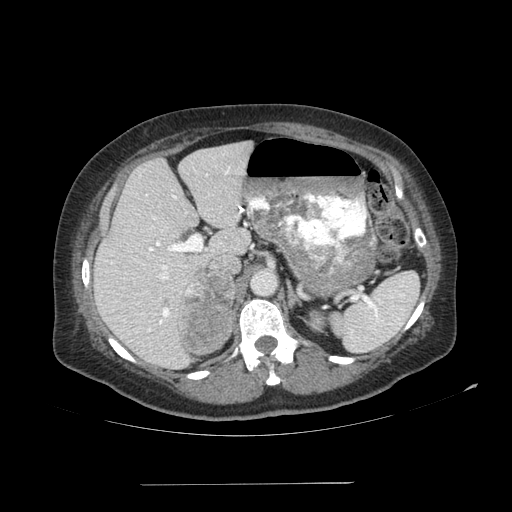
Contrast-enhanced abdominal CT, one axial slice. Position 68 of 113 along the scan axis. Reconstruction kernel SOFT. Soft-tissue window (W 400 / L 40 HU). 2.5 mm slice thickness. 512 × 512 image matrix. Patient: female, 67 years. Case-level facts recorded for this patient, not image findings: diagnosis: adrenocortical carcinoma; tumour side: right adrenal; tumour size at pathology: 9.8 cm; Ki-67 index: 59 %; stage (as recorded): 4.
Annotated regions visible in this slice (semi-automatic segmentation, software-assisted and operator-edited):
- mass: bounding box [x1, y1, x2, y2] px = [179, 272, 234, 354]